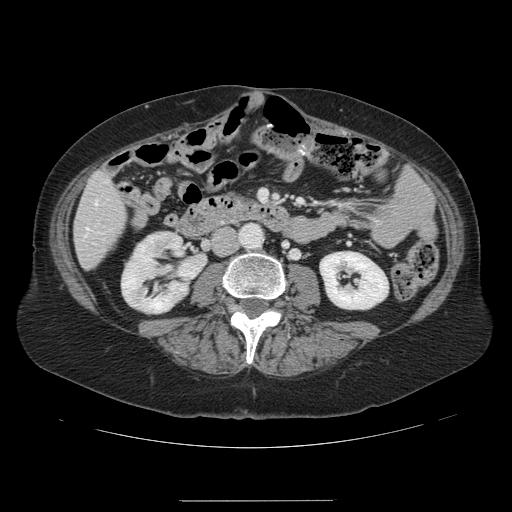
Contrast-enhanced abdominal CT, one axial slice; slice 27 of 141 in the series (ordered by position); soft-tissue window (W 400 / L 40 HU); 2.5 mm slice thickness; 512 × 512 image matrix, field of view 393 × 393 mm. Female patient, age 74 years. From the clinical record (not read from this slice): diagnosis: colorectal cancer liver metastases, imaged before liver resection; multiple liver metastases: yes; largest metastasis: 7 cm; disease in both lobes: yes.
Annotated regions visible in this slice (outlined manually by an expert reader):
- hepatic veins: bounding box [x1, y1, x2, y2] px = [86, 201, 97, 230]
- liver: [75, 173, 126, 268]
- planned liver remnant (the part of the liver to remain after resection): [75, 173, 125, 268]